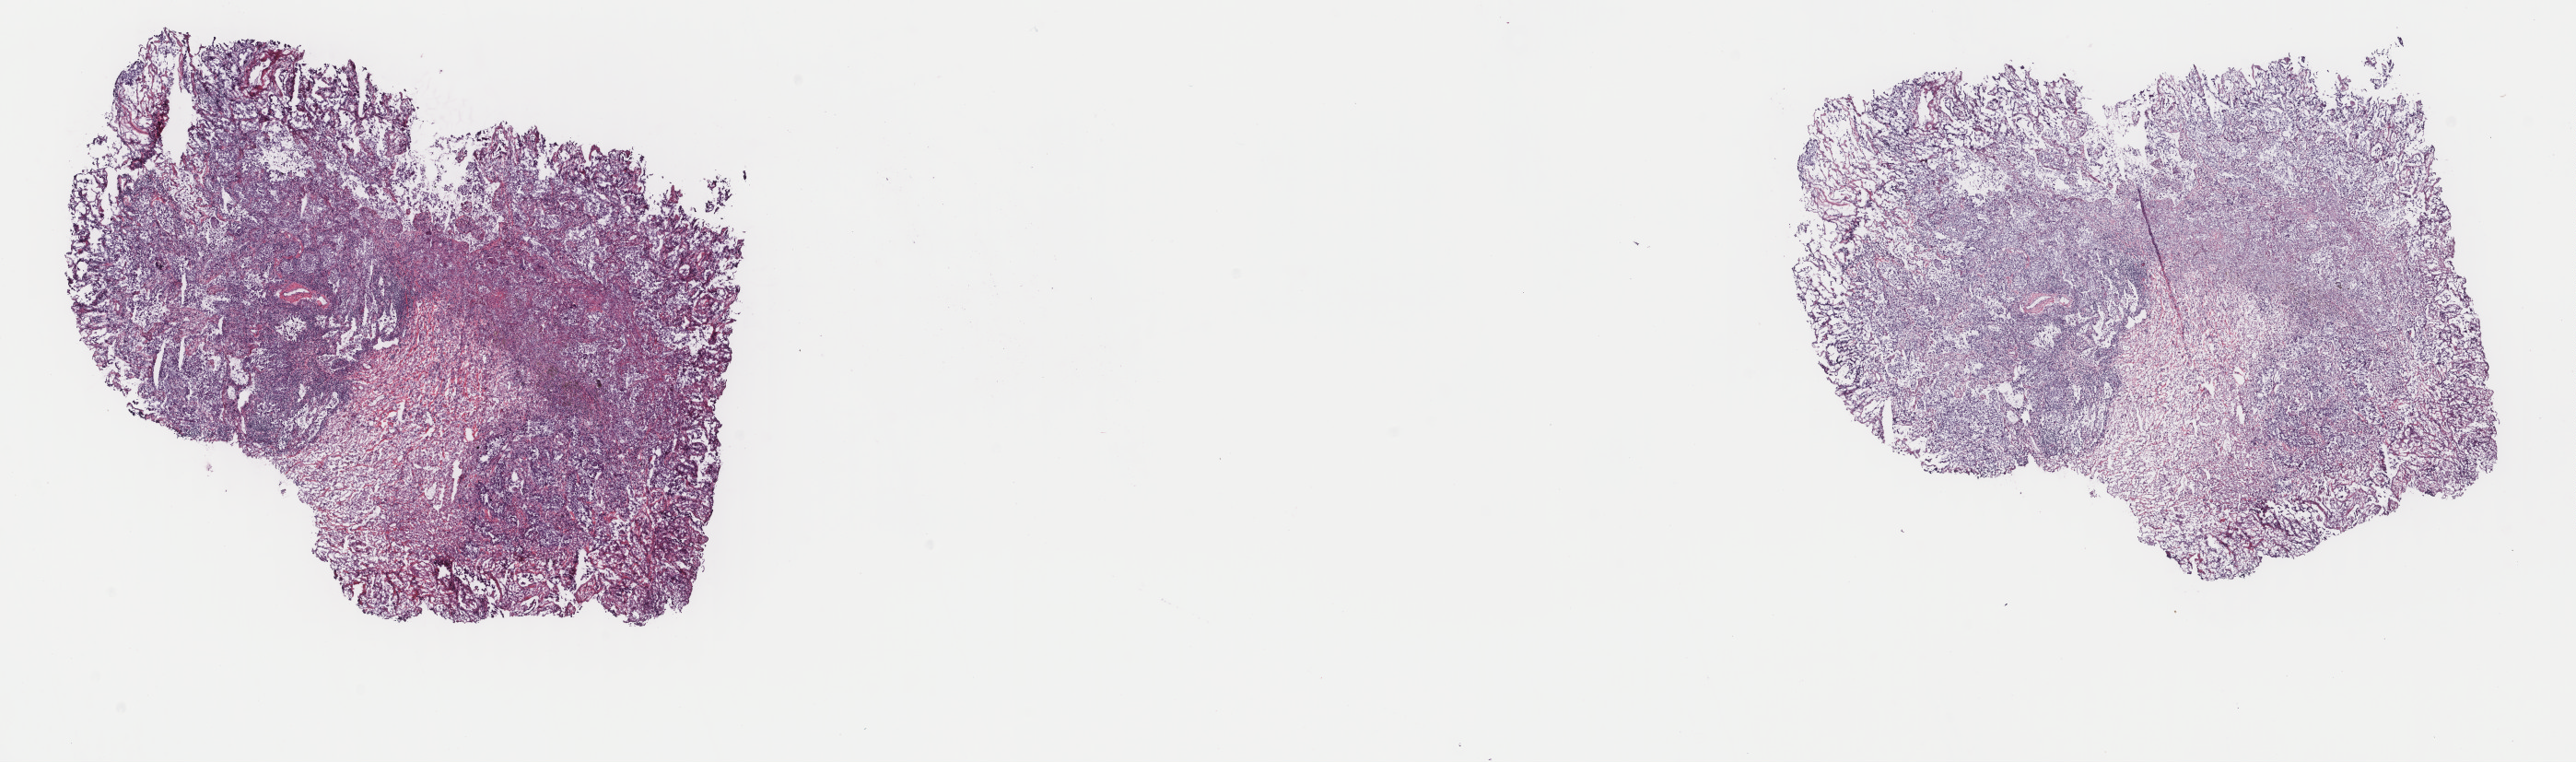
H&E-stained whole-slide image, a low-resolution overview of the entire scanned area, about 22.2 x 6.6 mm (slide scanned at 40x), frozen section from the top of the tissue portion, lung, primary tumour sample. Female, age 73 years at initial diagnosis. Pathologist review of this section (percent, as recorded): tumour cells 80%, tumour nuclei 75%, normal cells 20%, stromal cells 0%, necrosis 0%. Infiltration values recorded for this section: lymphocyte infiltration 2%, monocyte infiltration 5%, neutrophil infiltration 0%.
AJCC pathologic stage: IA (7th edition). Laterality: right. TNM: T1 N0 M0. Histologic diagnosis: Adenocarcinoma, NOS (upper lobe, lung).